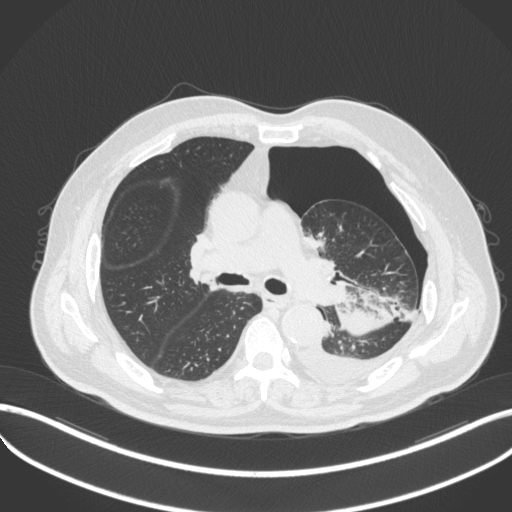
Chest CT, one axial slice; position 315 of 466 along the scan axis; lung window (W 1500 / L -600 HU); 1 mm slice thickness; 512 × 512 image matrix, field of view 400 × 400 mm. Patient: male, 76 years. Case-level facts recorded for this patient, not image findings: clinical TNM (as recorded): T3 N0 M1b.
Annotated regions visible in this slice (bounding box drawn by a radiologist):
- lung tumour (recorded histology: adenocarcinoma): bounding box <328,278,408,338> (left, top, right, bottom; pixels)